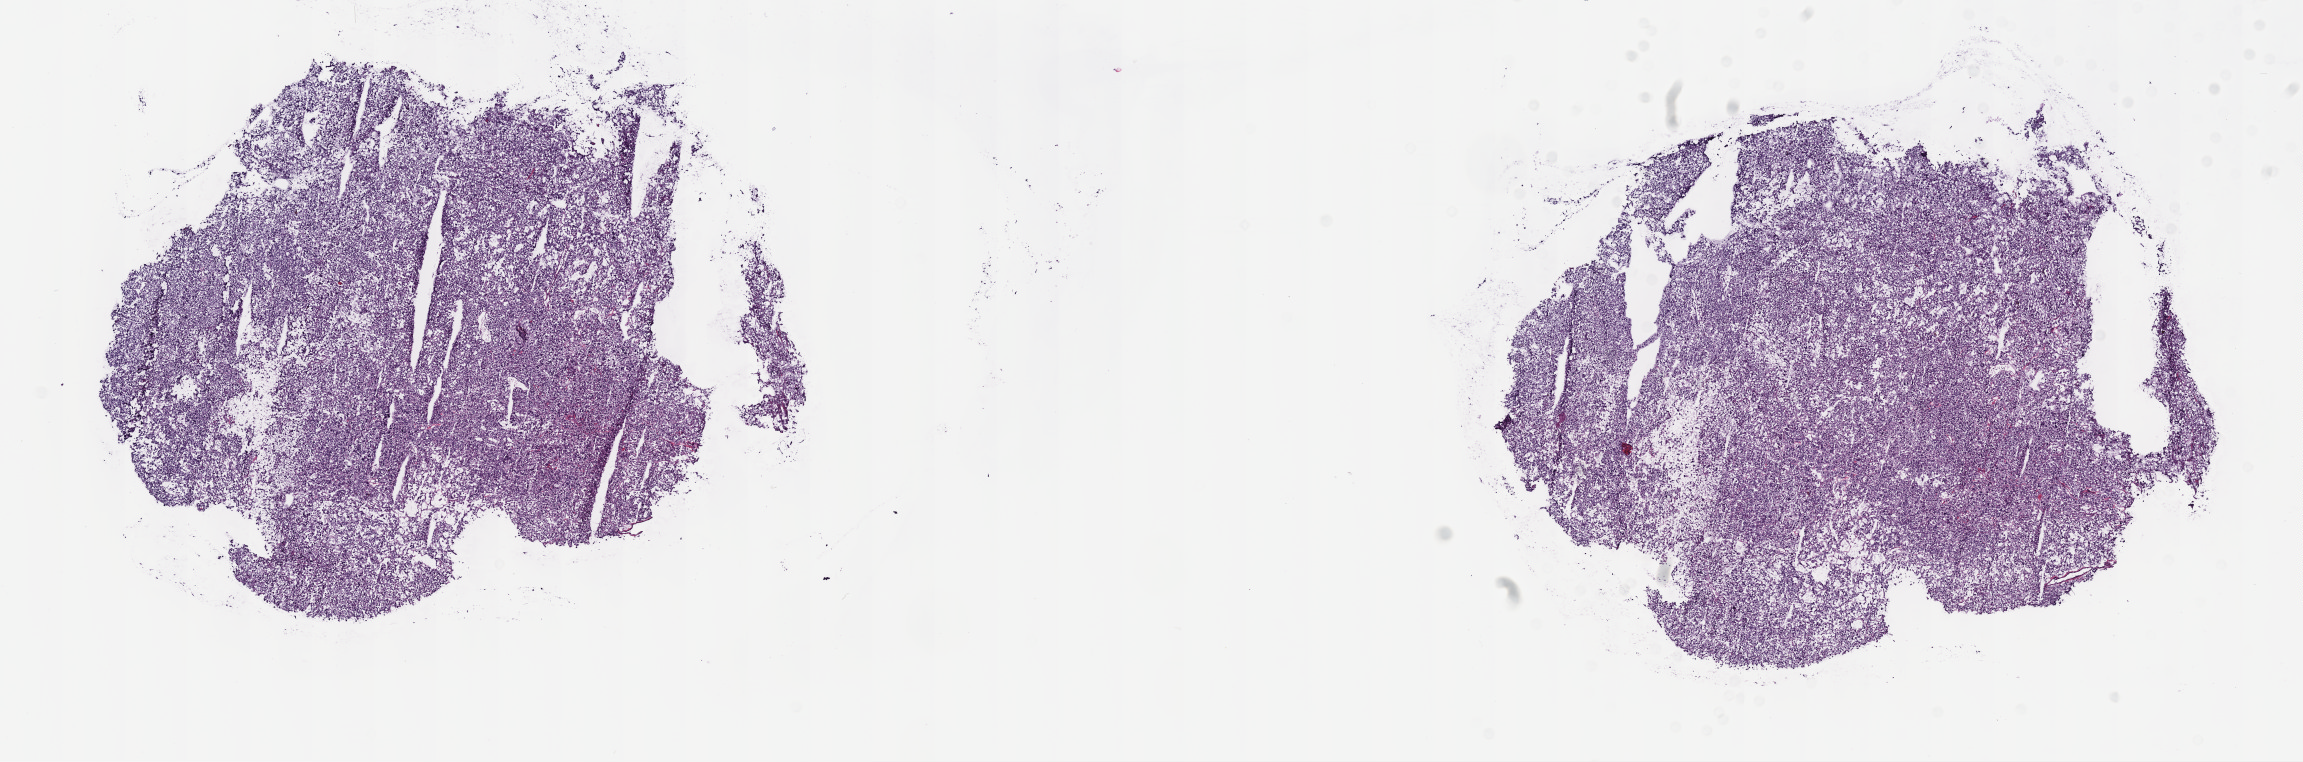
Digitized H&E tissue section (whole slide) — shown as a low-resolution overview of the whole scanned area (about 18.6 x 6.2 mm, from a 40x scan); frozen section; sample: primary tumour, adrenal gland. Female patient; age at initial diagnosis 73 years. Pathologist review of this section (percent, as recorded): tumour cells 100%, tumour nuclei 80%, normal cells 0%, stromal cells 0%, necrosis 0%. Infiltration values recorded for this section: lymphocyte infiltration 1%, monocyte infiltration 0%, neutrophil infiltration 0%.
Diagnosis: Pheochromocytoma, NOS.